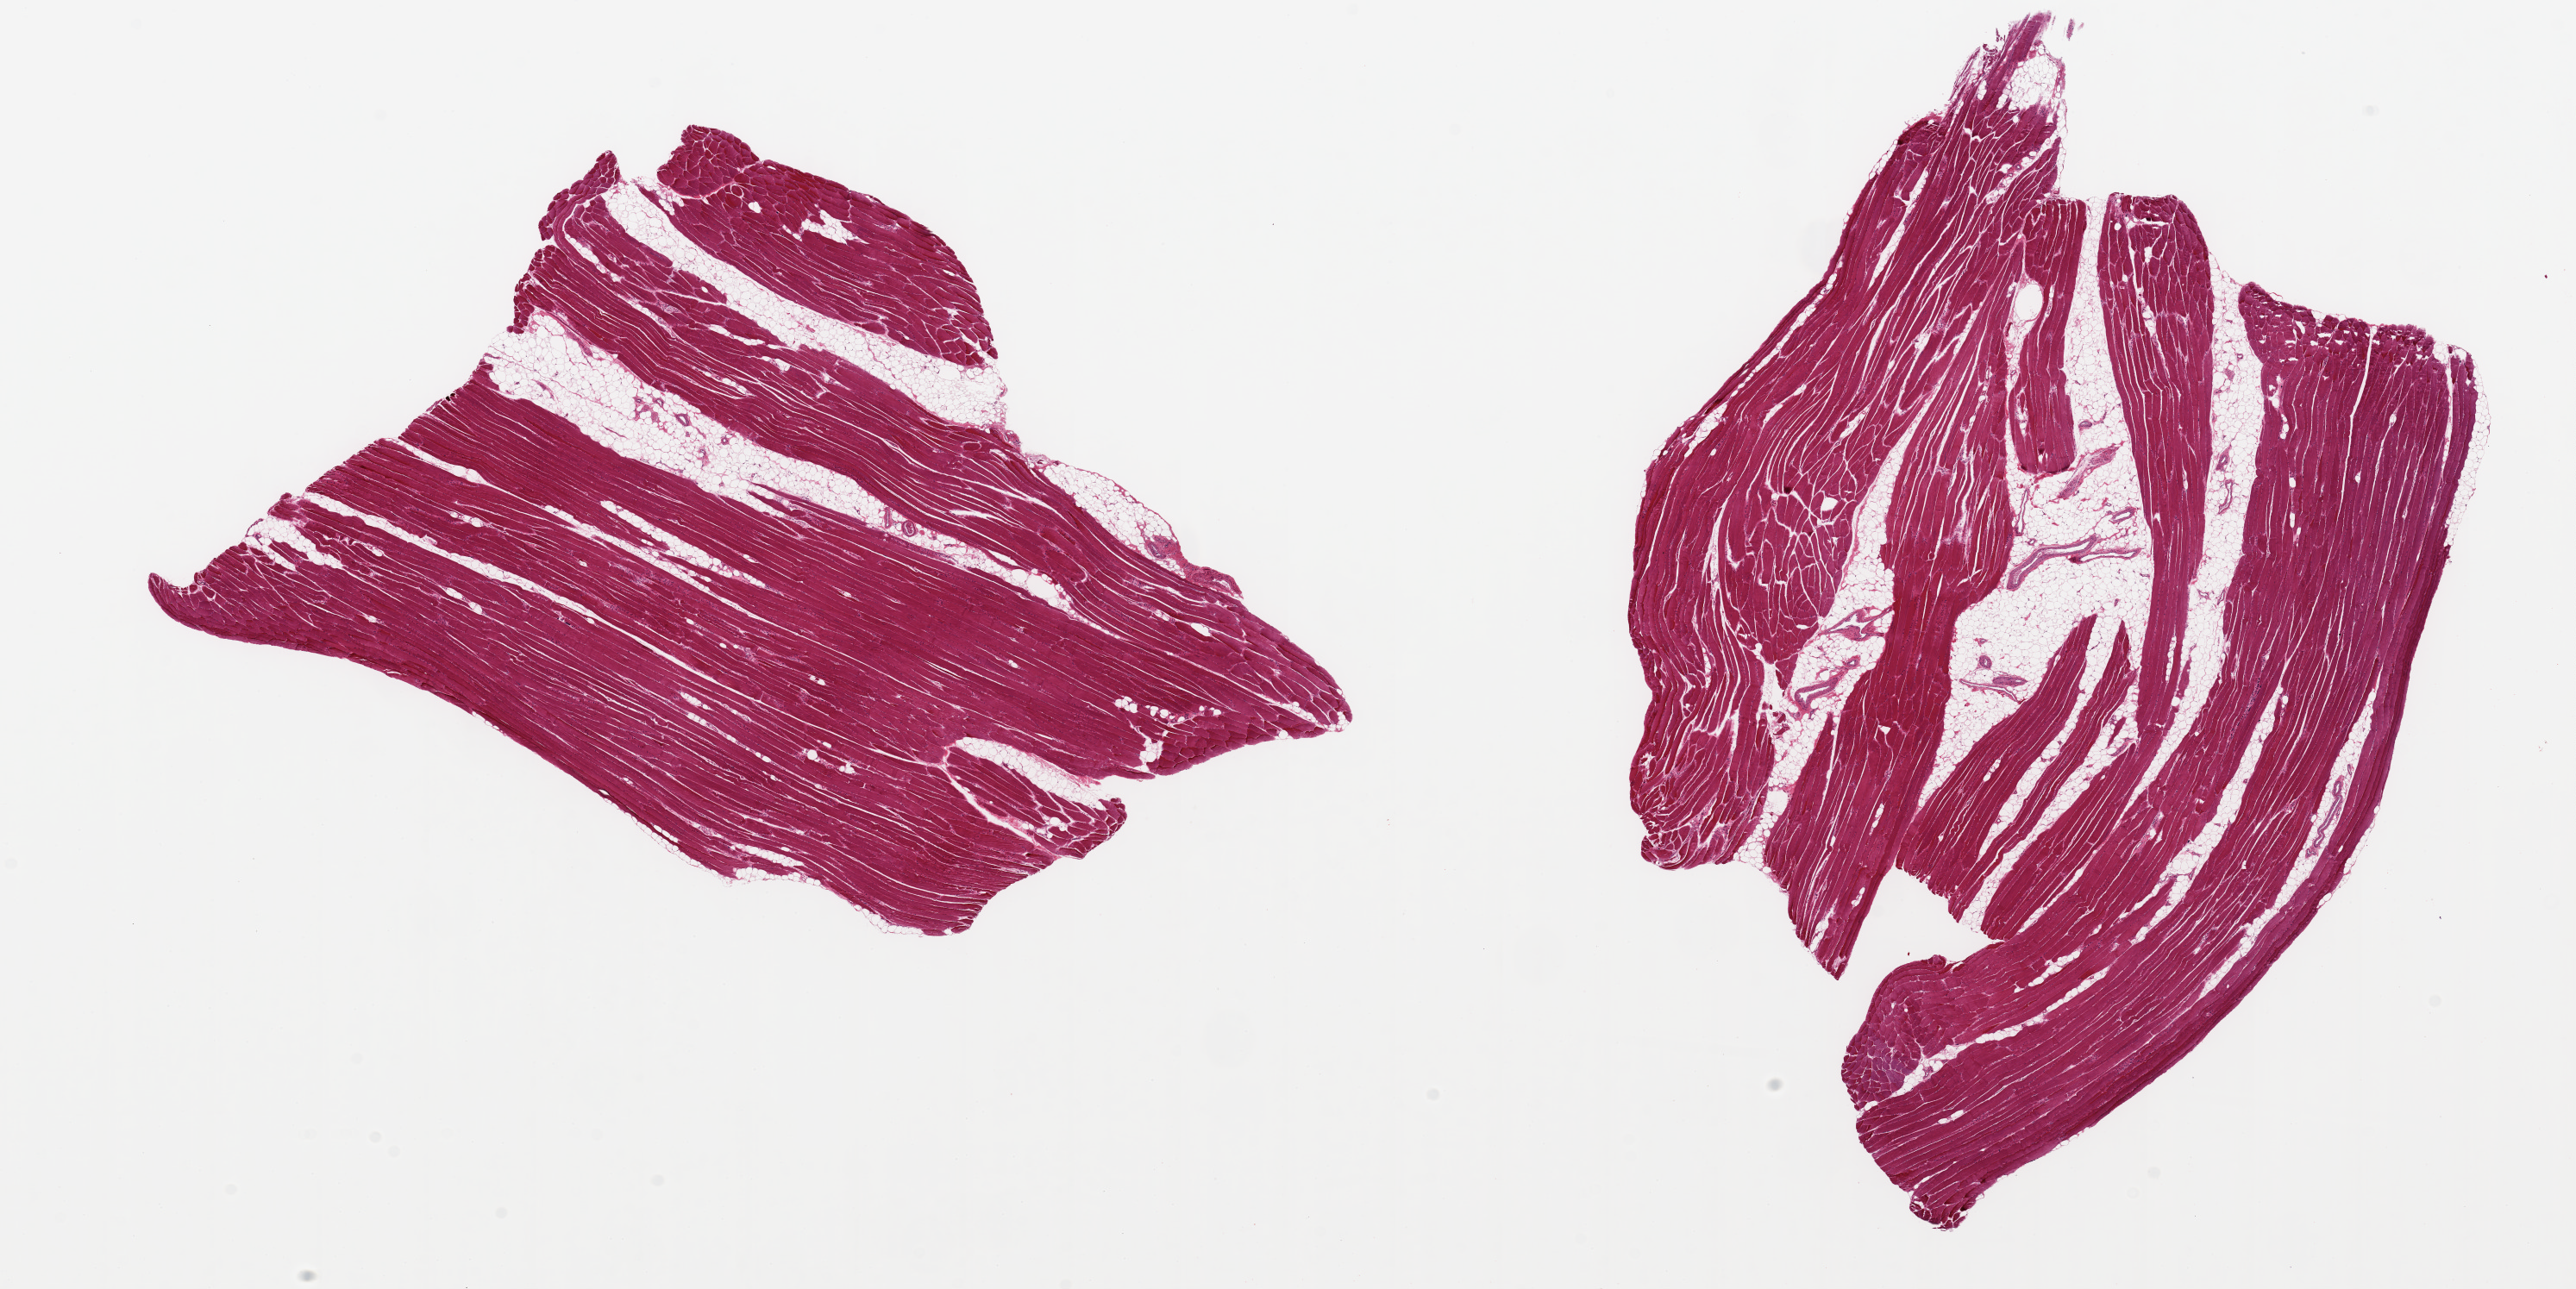
Whole-slide image, hematoxylin and eosin (H&E) stain, brightfield, whole scanned area (about 23.6 x 11.8 mm, slide scanned at 20x) shown as a low-resolution overview; PAXgene-fixed paraffin-embedded (PFPE) section; section of skeletal muscle (target tissue); donor tissue sample.
Pathologist's review note for this sample: 2 pieces, 9x7 & 10x7mm; ~10-20% interstitial fat.